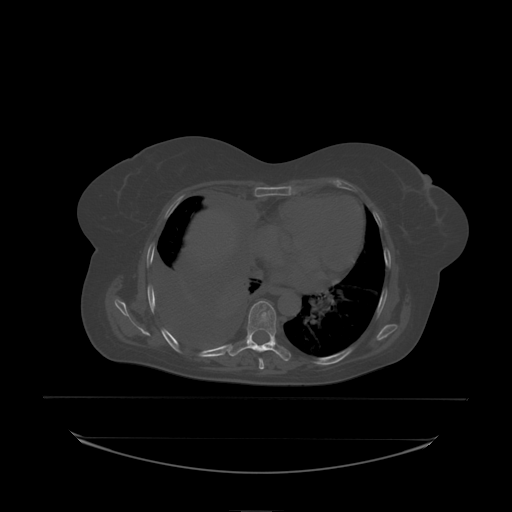
CT including the spine, one axial slice; slice 134 of 242 in the series (ordered by position); bone window (W 1800 / L 400 HU); 2.5 mm slice thickness; 512 × 512 image matrix, field of view 500 × 500 mm. Female patient, age 53 years. From the clinical record (not read from this slice): primary cancer: lung; vertebrae with lytic lesions (as recorded): T7, L1.
Outlined on this slice (semi-automatic segmentation, software-assisted and operator-edited):
- T8 vertebra: box from (x=247, y=301) to (x=277, y=338) px